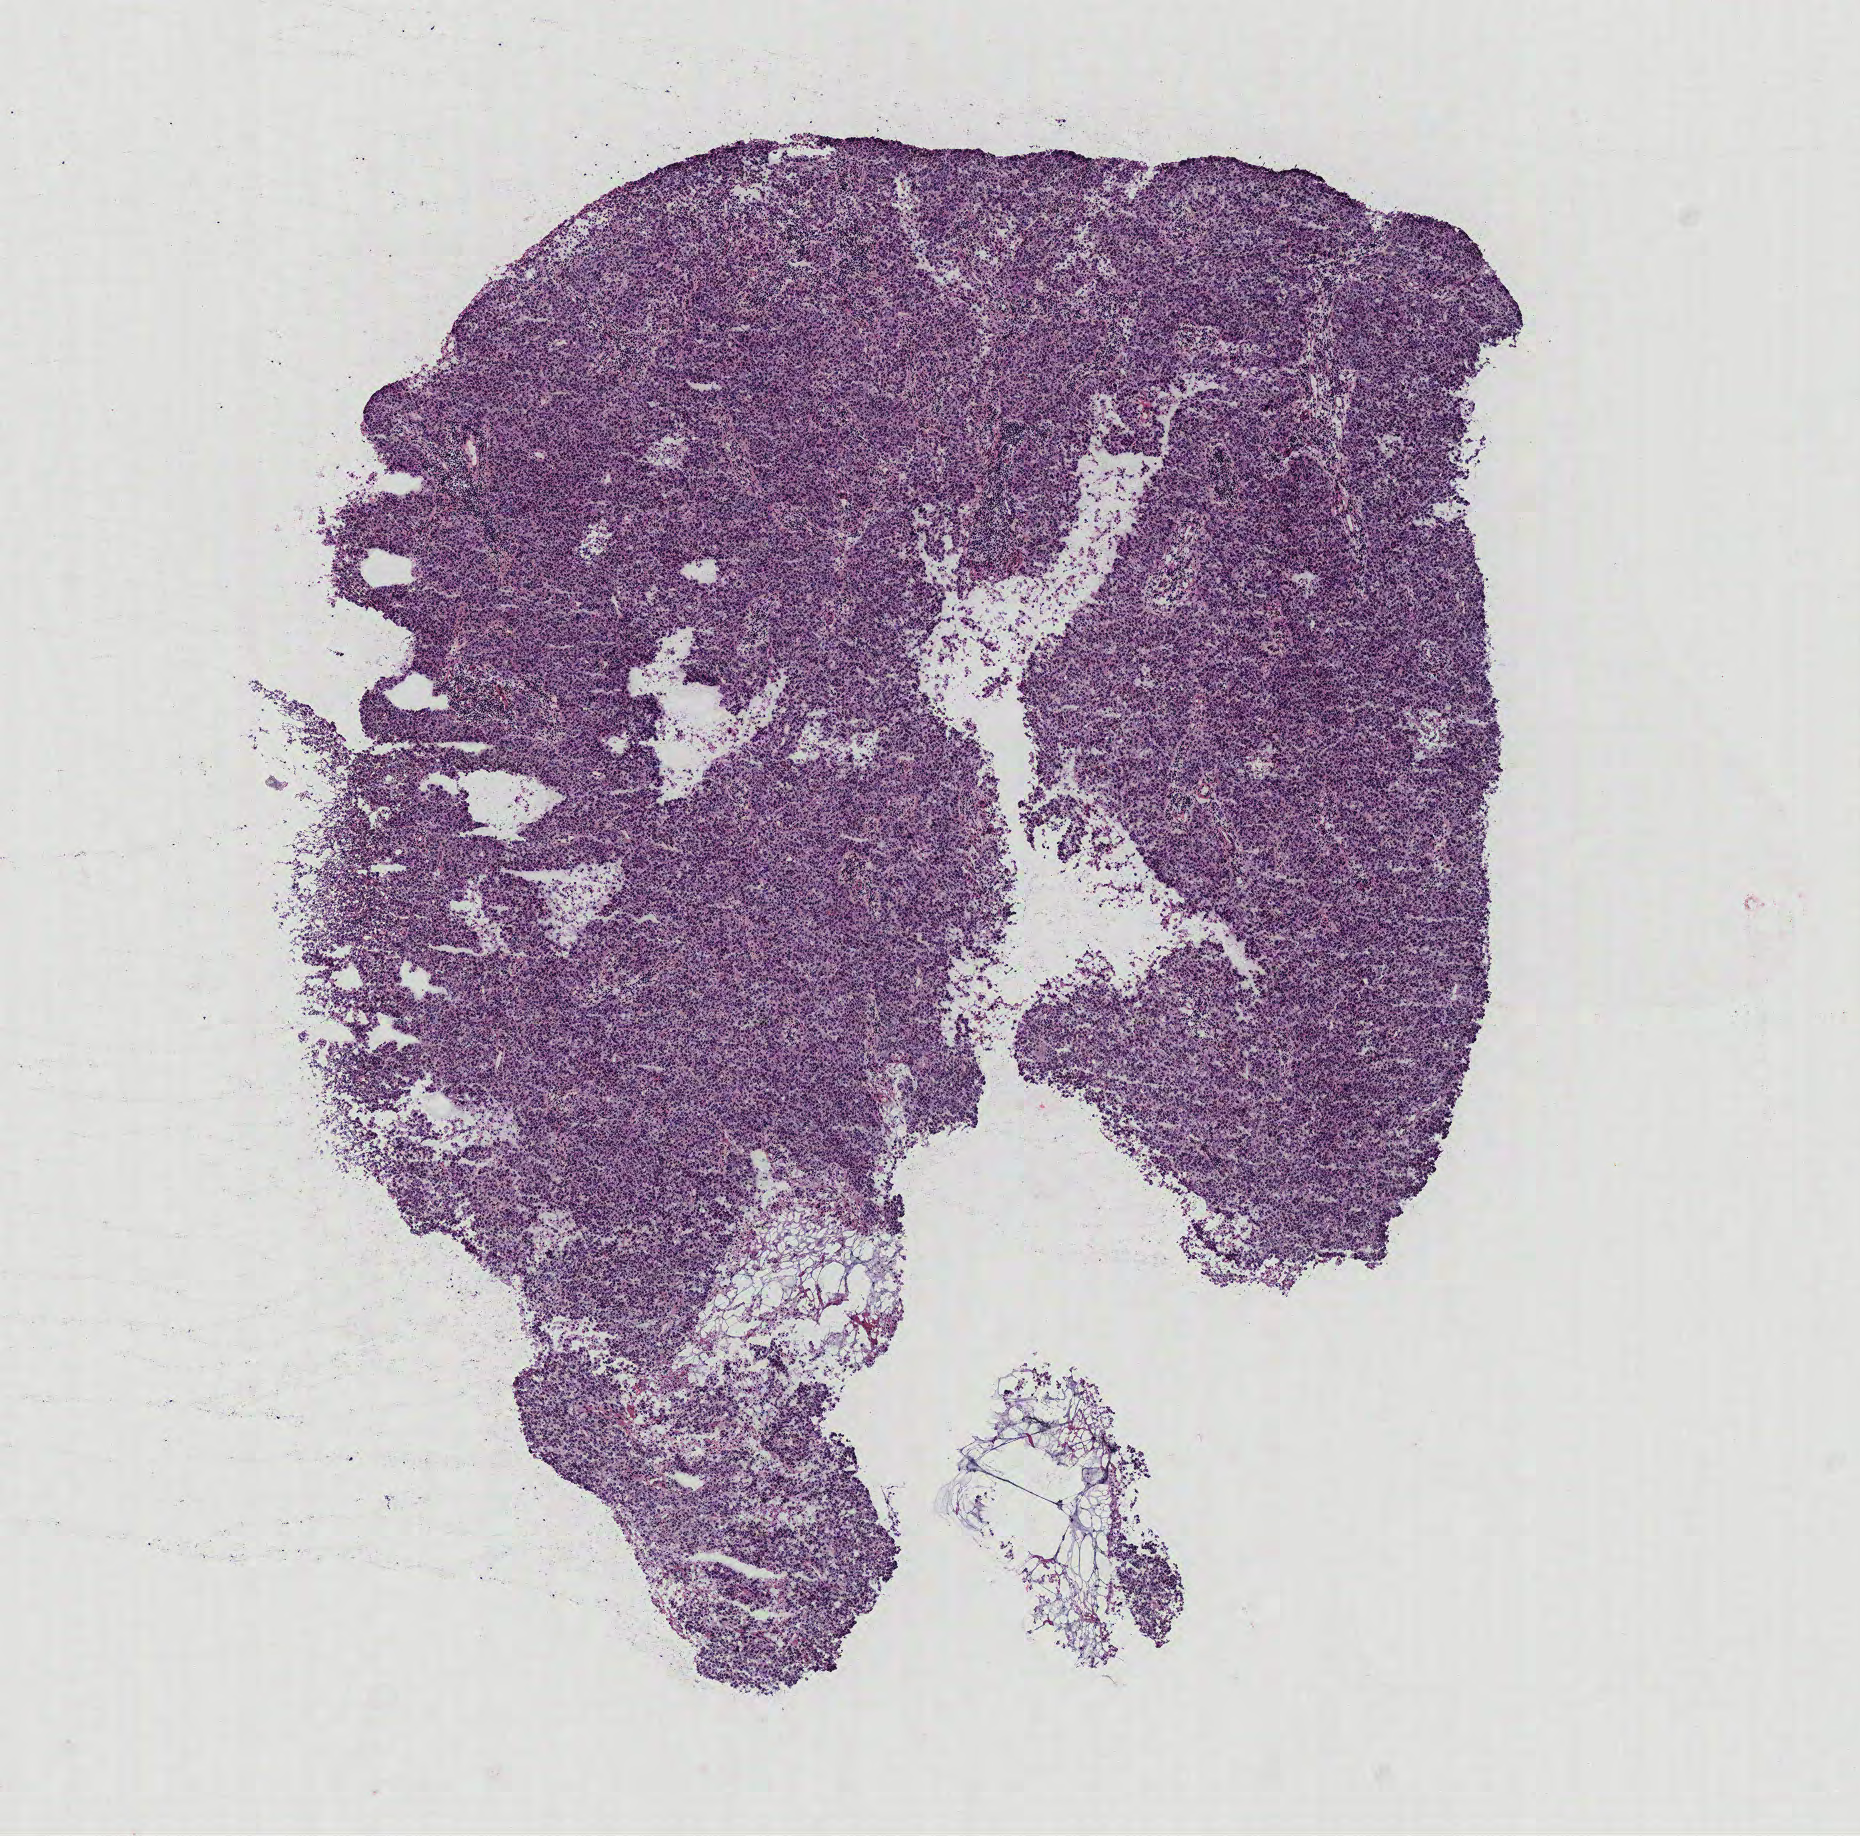
Whole-slide histology image, H&E-stained — low-resolution overview of the scanned area, about 7.4 x 7.3 mm, breast, tissue type not recorded. 61-year-old female patient.
Patient diagnosis: Infiltrating duct carcinoma, NOS.